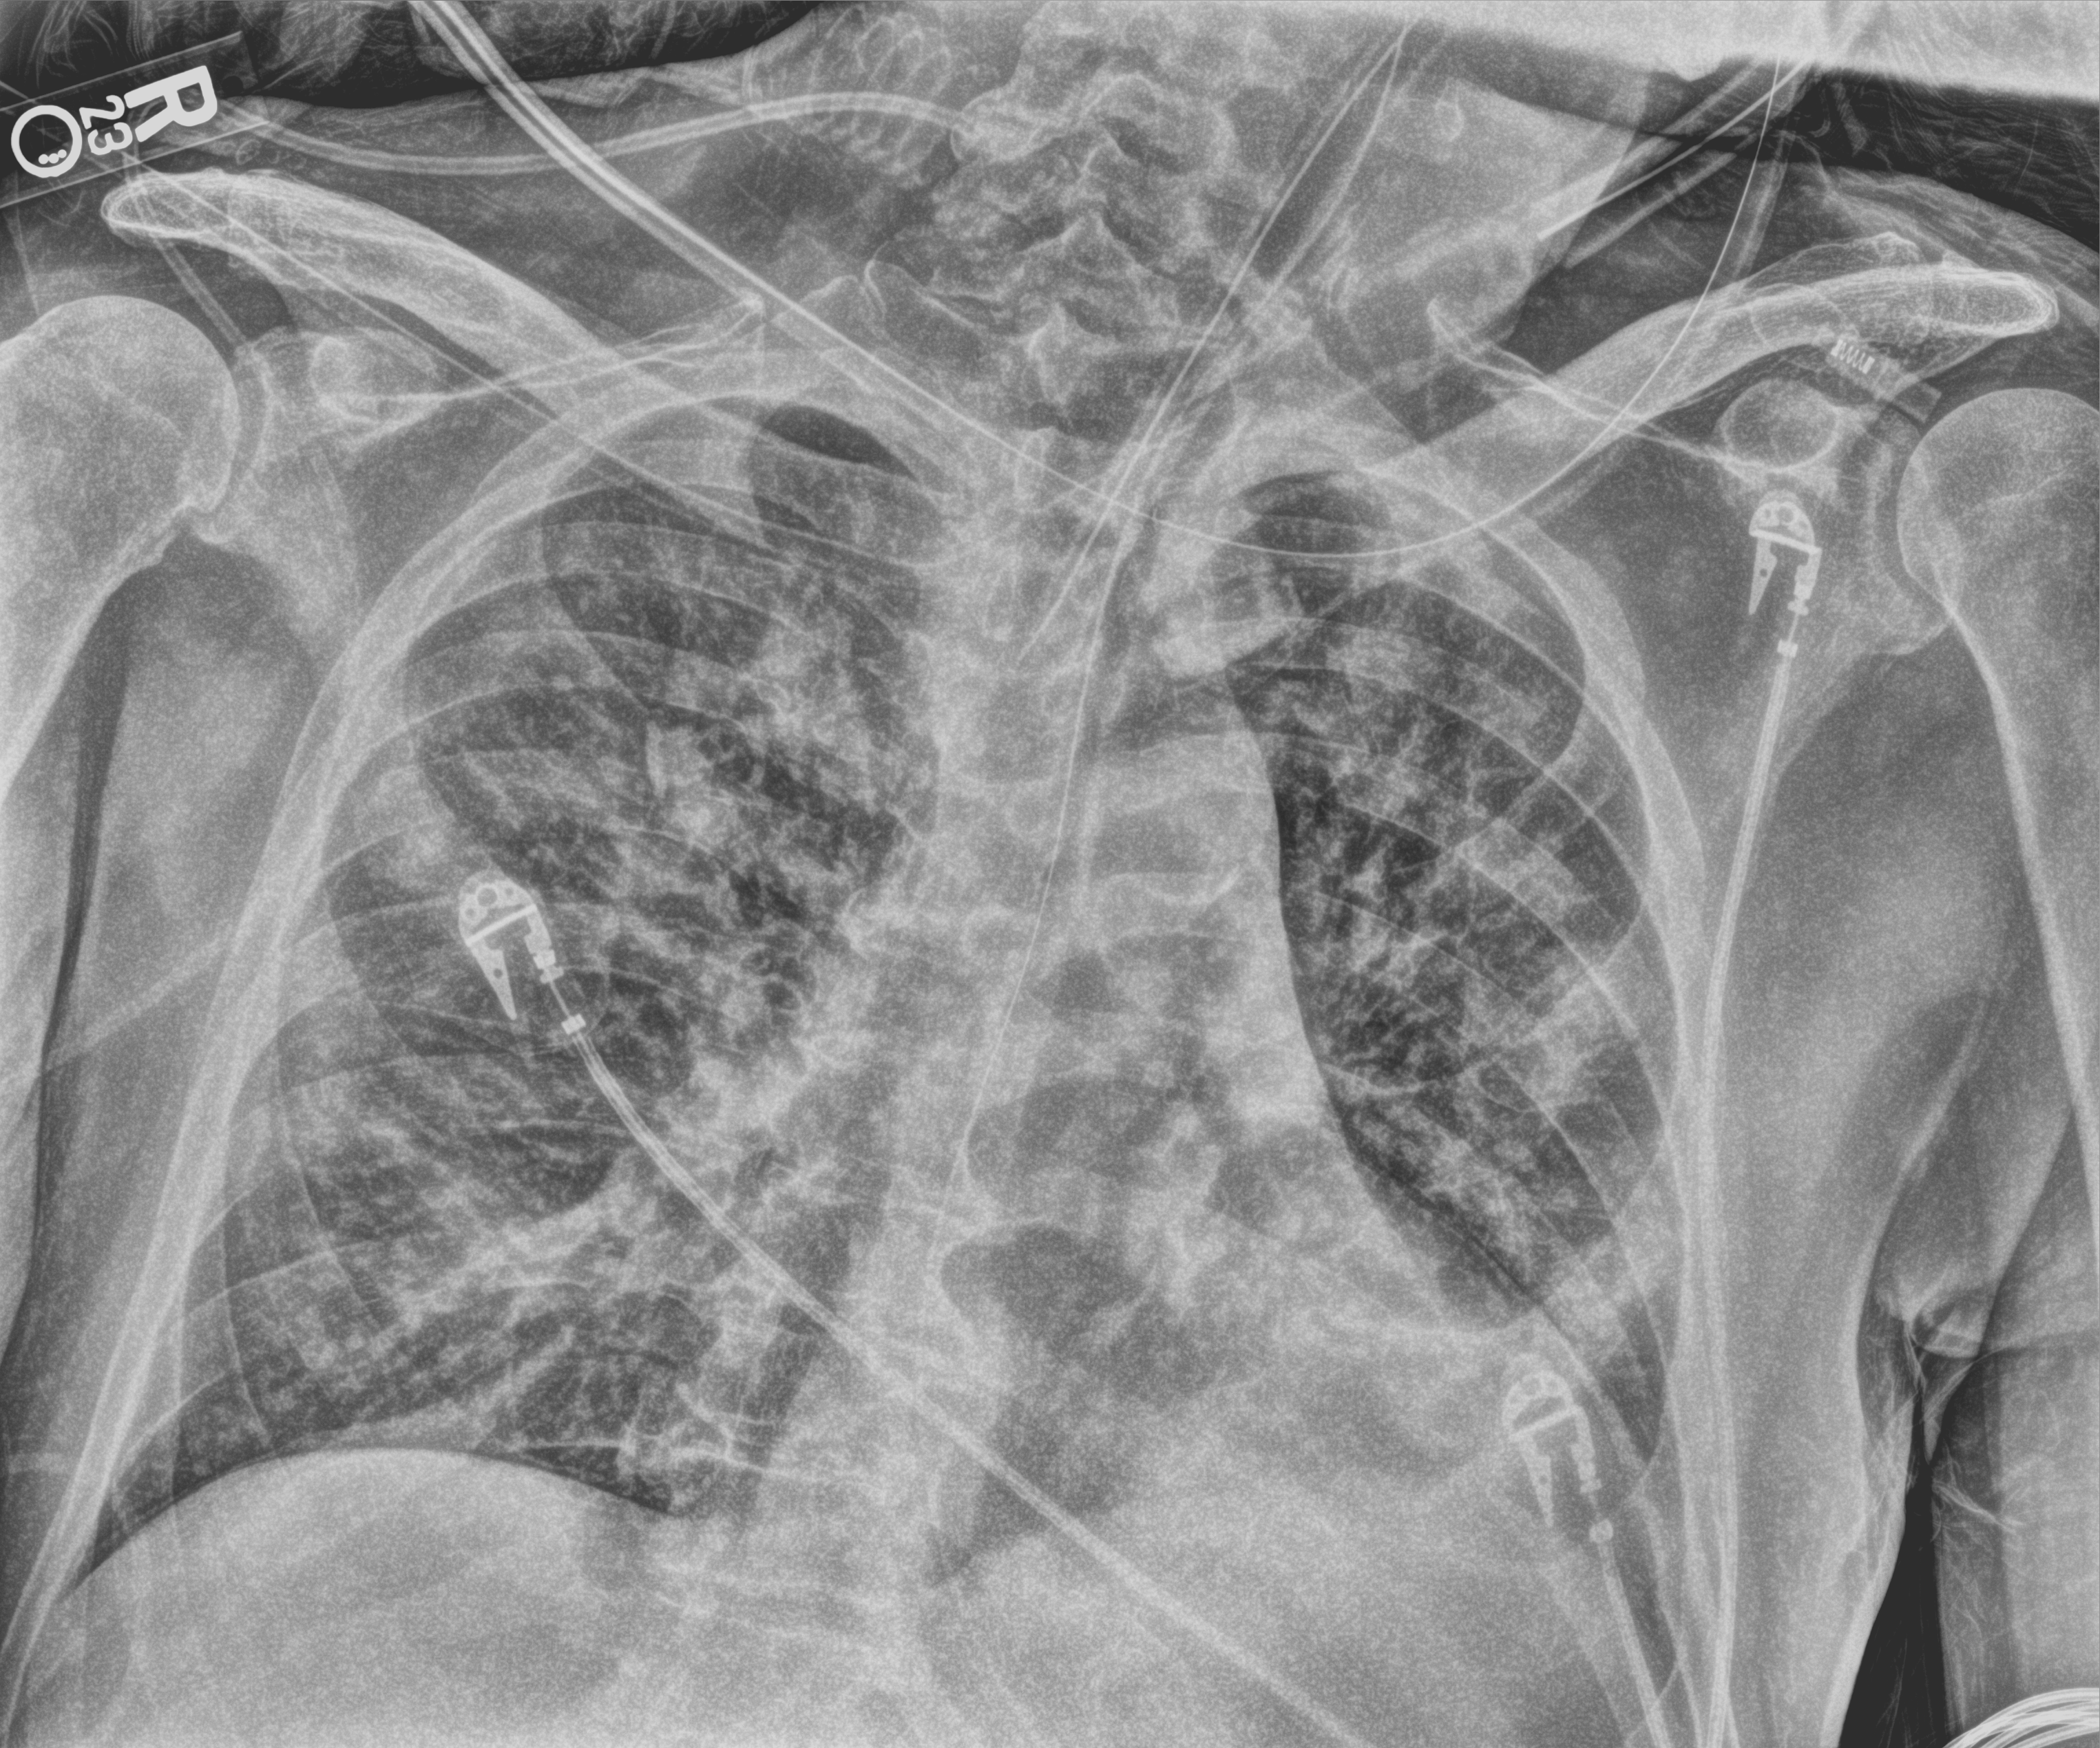
Portable chest radiograph; anteroposterior (AP) projection. Male patient hospitalised with COVID-19, age 60–74 years.
Admission-level facts for this patient (not findings on this image; timing relative to this image not recorded): diabetes (admission record): yes.